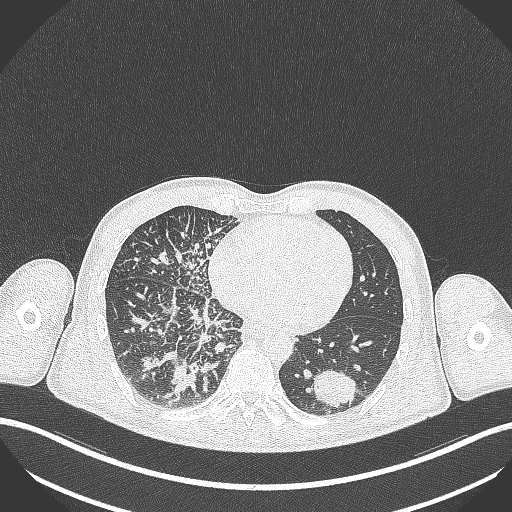
Chest CT, one axial slice. Position 110 of 348 along the scan axis. Reconstruction kernel B70f. 120 kVp. Lung window (W 1500 / L -600 HU). 1 mm slice thickness. 512 × 512 image matrix, field of view 400 × 400 mm. Male patient, age 49 years. From the clinical record (not read from this slice): clinical TNM (as recorded): T2b N1 M0.
Structures marked on this image (bounding box drawn by a radiologist):
- lung tumour (recorded histology: adenocarcinoma): bounding box [x1, y1, x2, y2] px = [310, 370, 357, 409]